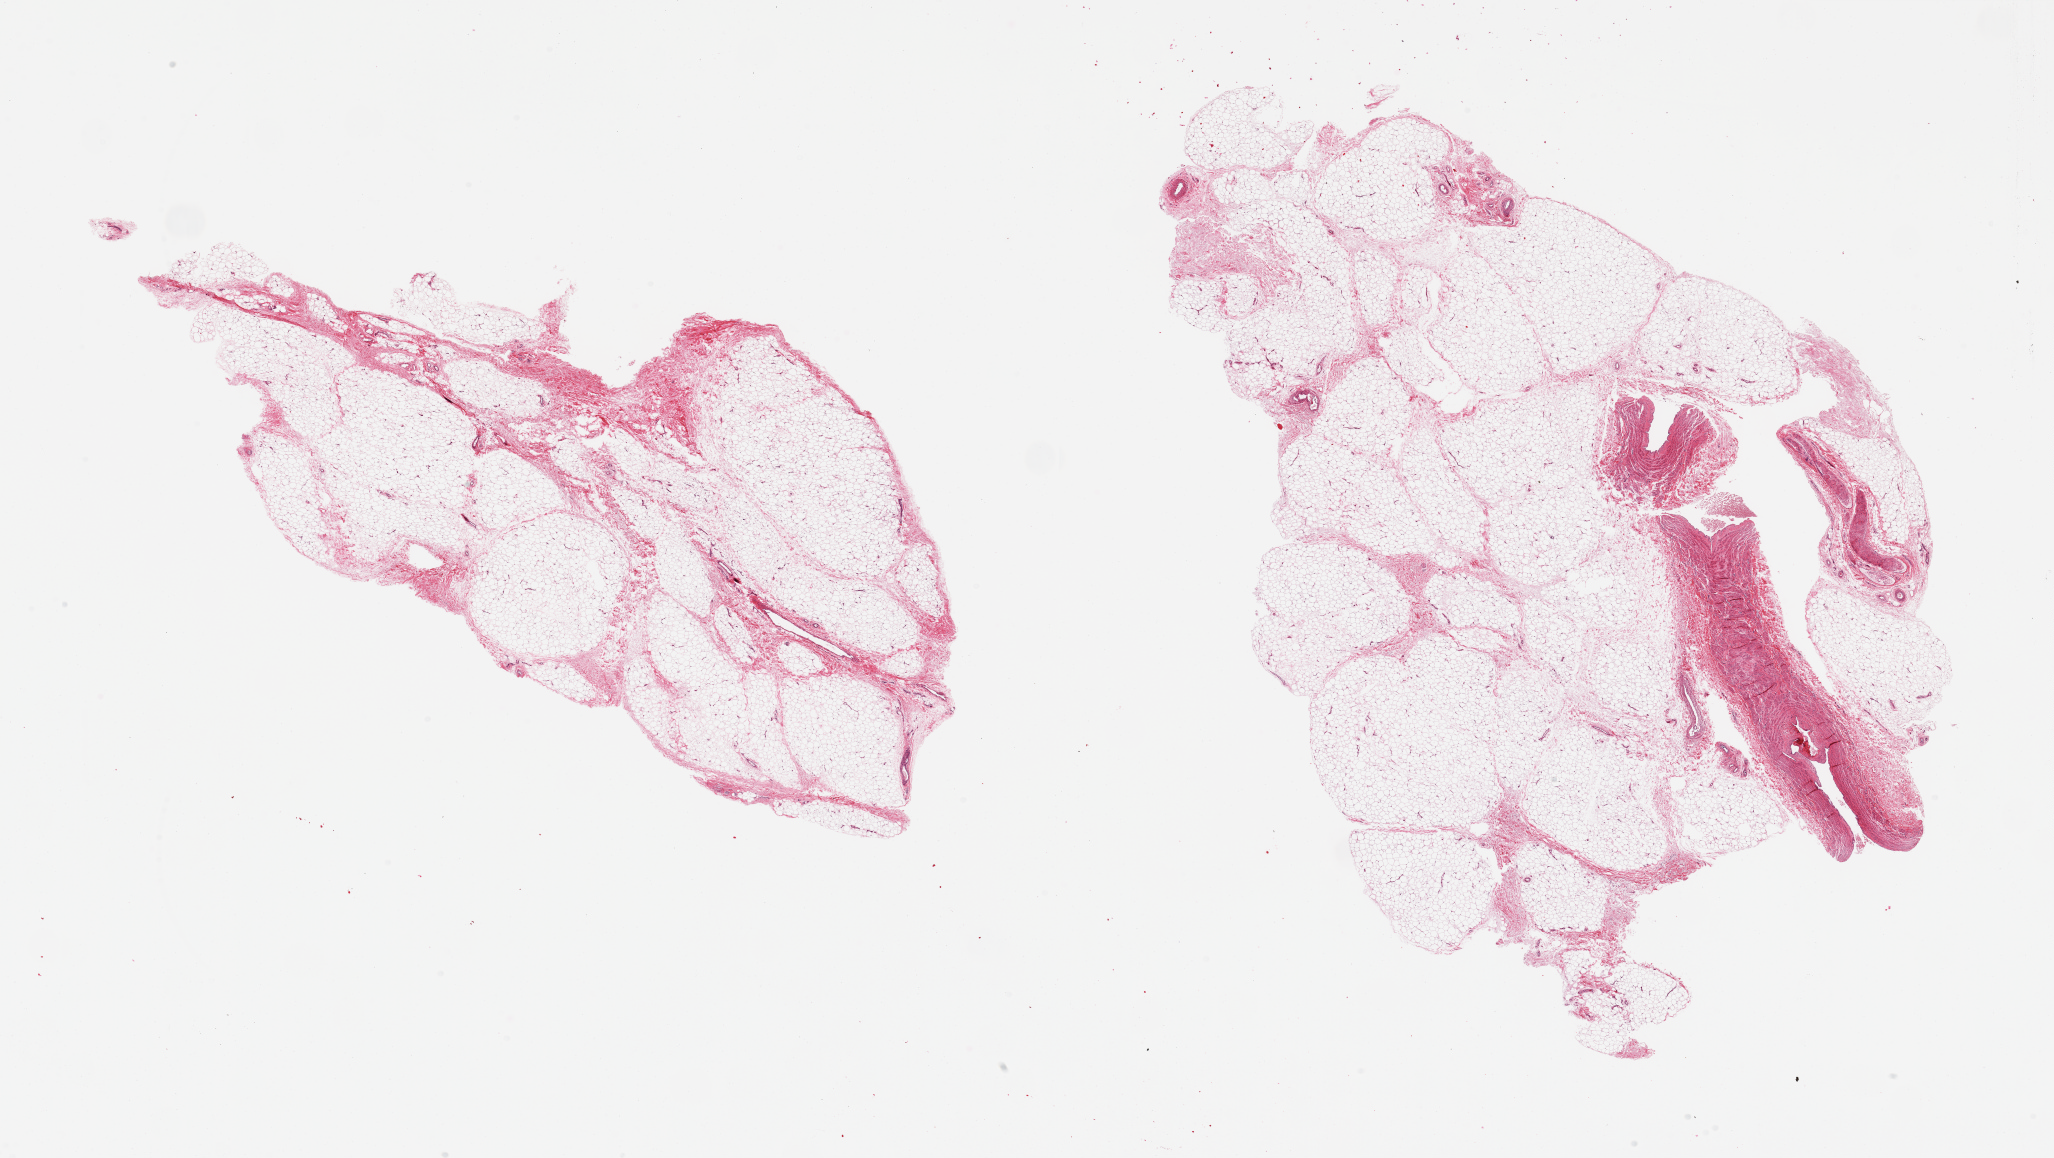
H&E whole-slide image, whole scanned area (about 32.5 x 18.3 mm) shown as a low-resolution overview; PAXgene-fixed paraffin-embedded (PFPE) section; target tissue: adipose tissue; tissue donor sample. Donor: male.
Reviewer comment on this tissue sample: 2 pieces, fascia/vascular elements are ~15% tissue.